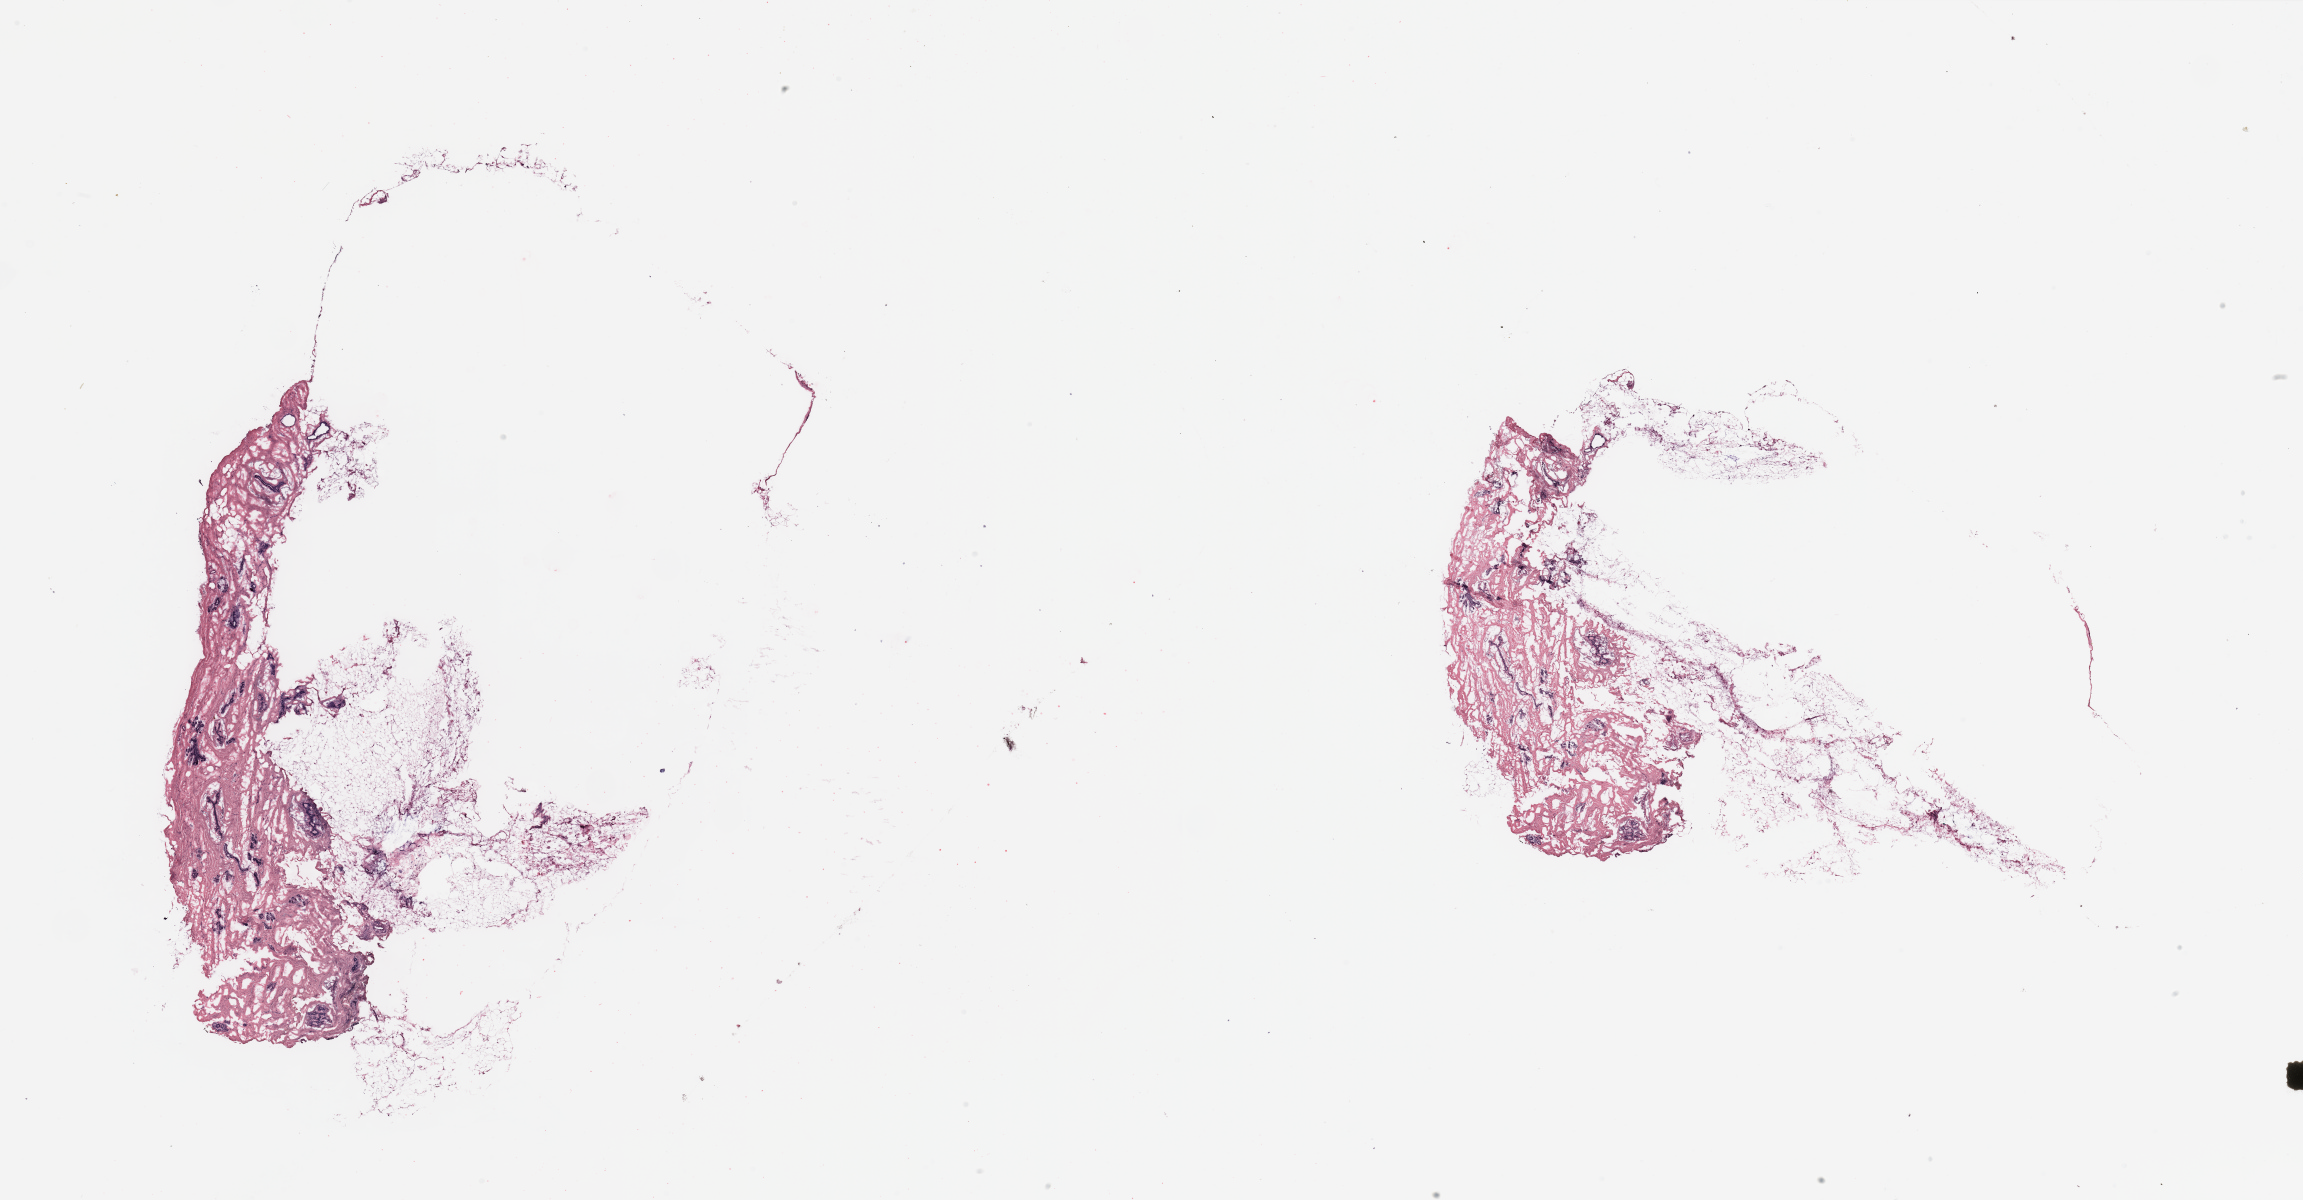
Whole-slide histology image, H&E-stained, whole scanned area (about 36.4 x 19.0 mm) shown as a low-resolution overview, breast, tumour tissue. 71-year-old female patient.
Histologic diagnosis: Infiltrating duct carcinoma, NOS.